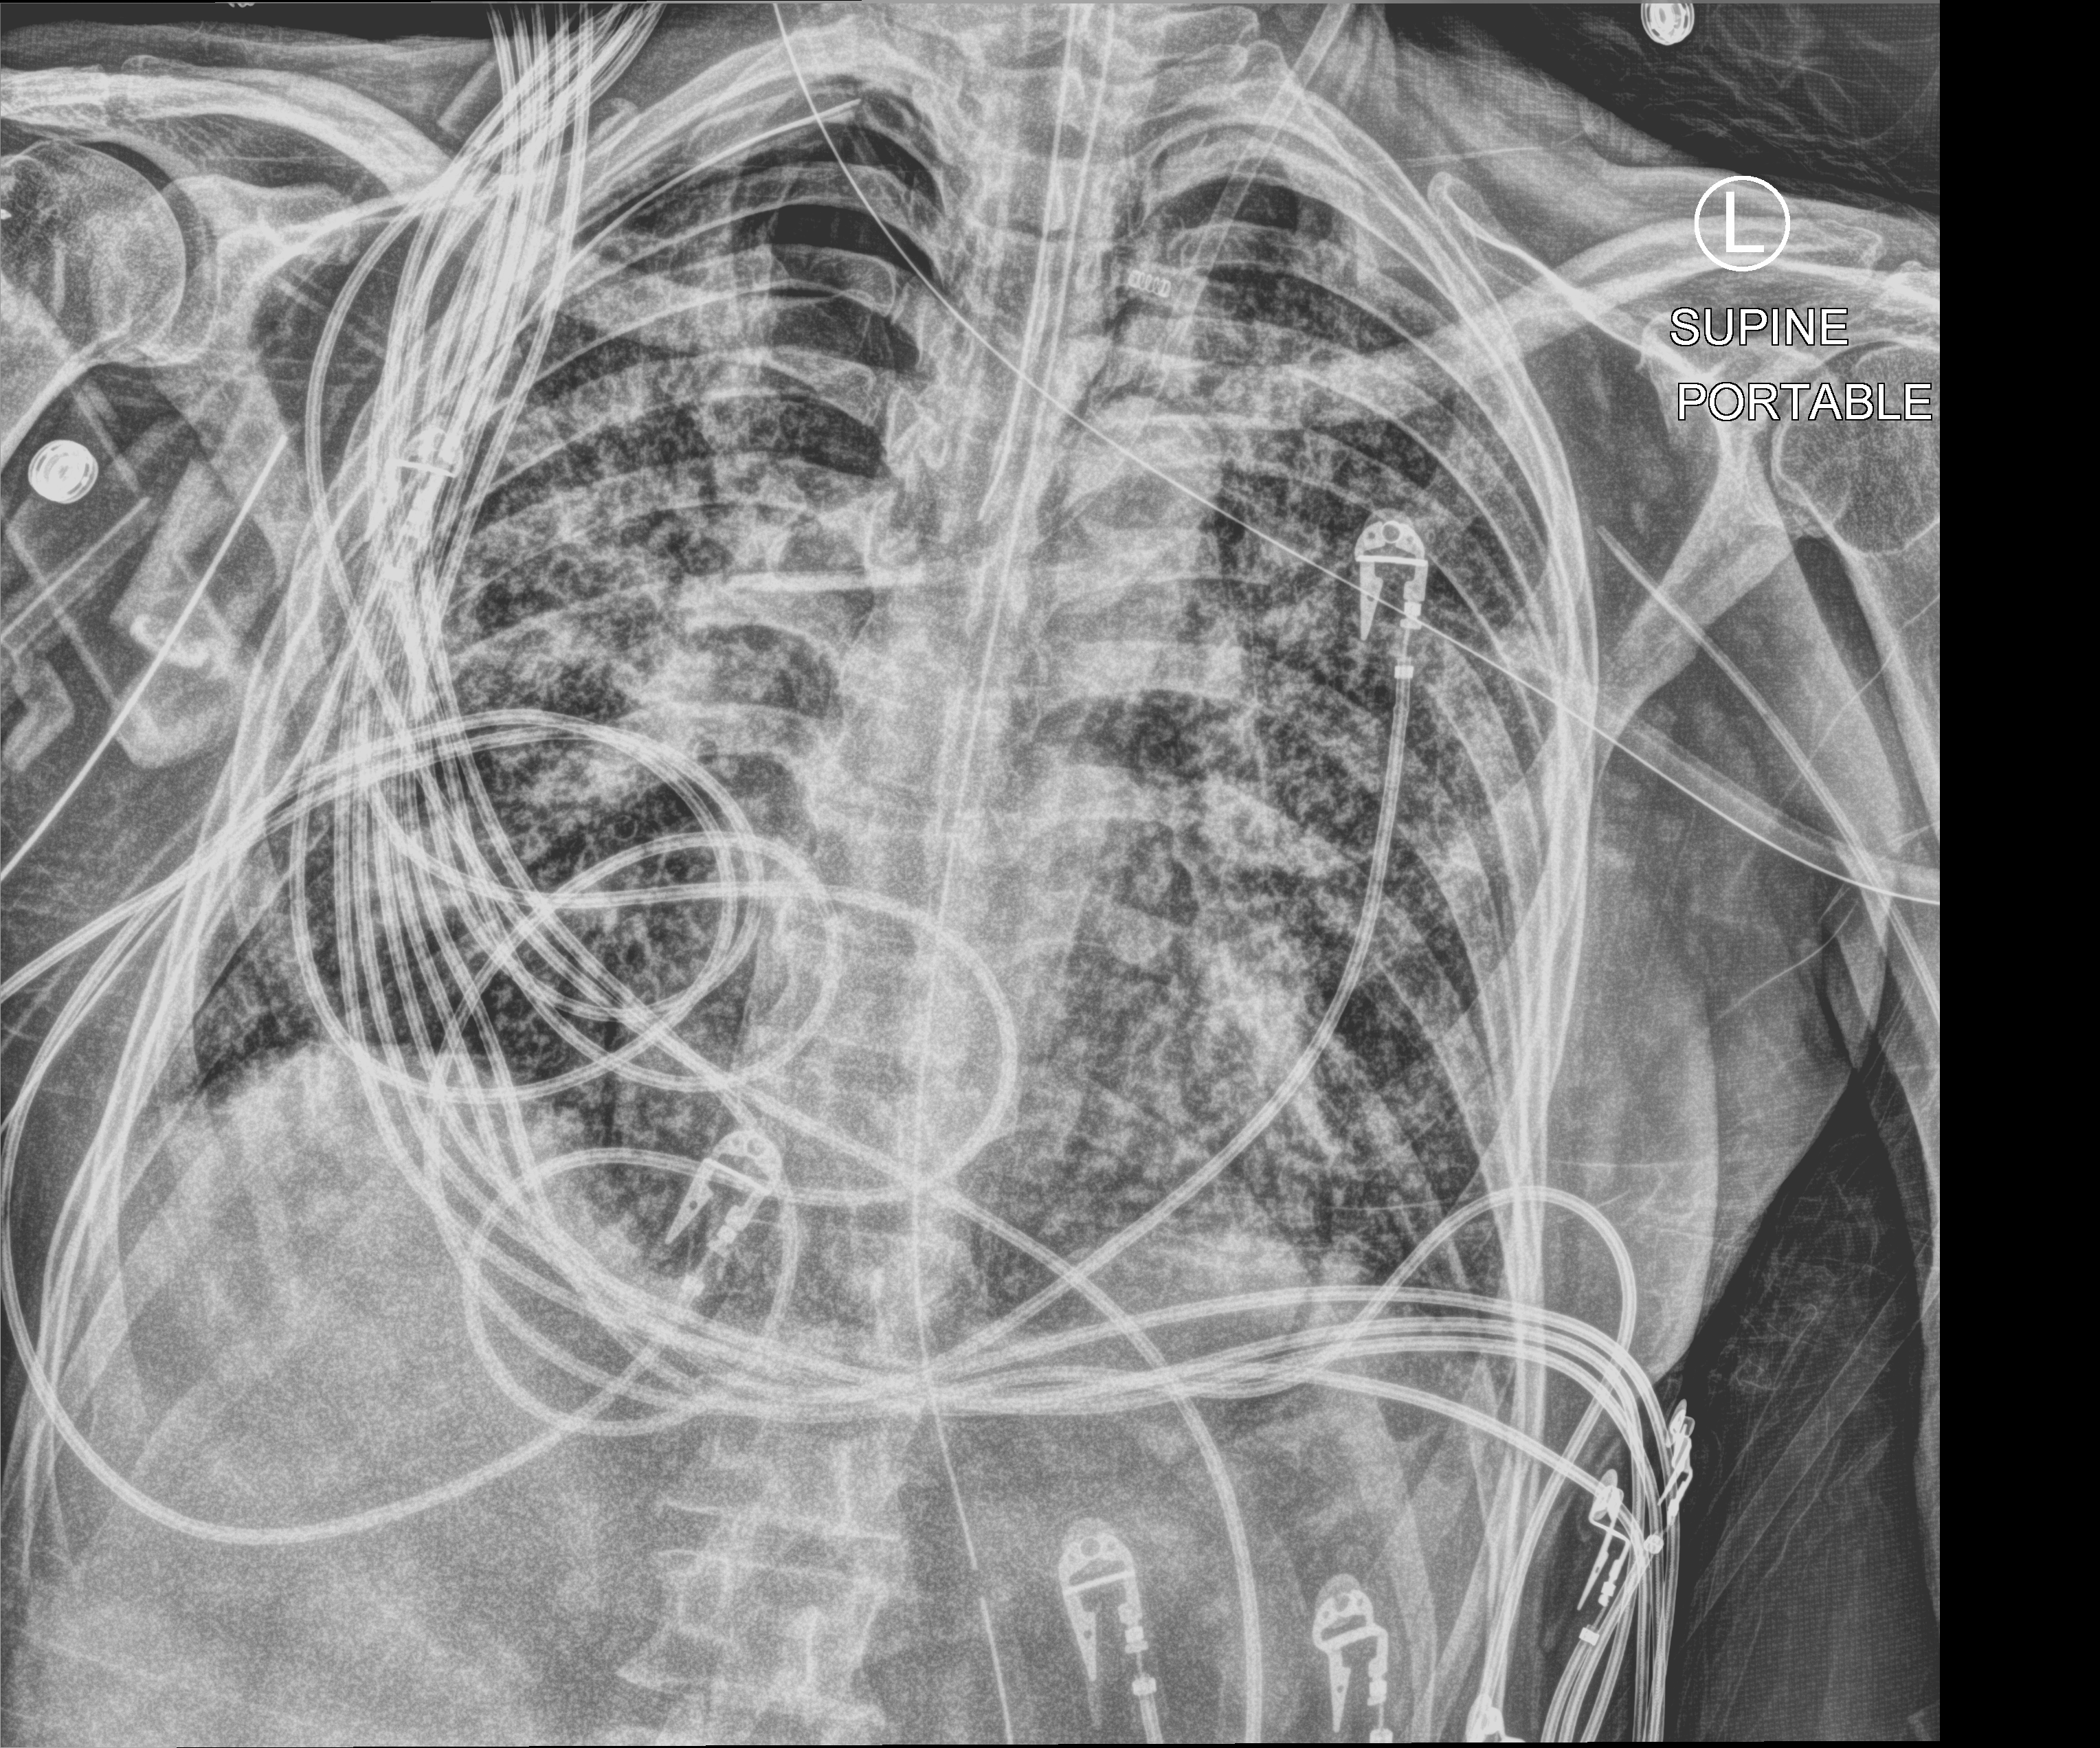
Chest X-ray (portable). Male patient hospitalised with COVID-19, age 60–74 years.
Hospital-stay facts (about this admission, not read from this image; timing relative to this image not recorded): COPD (admission record): no; chronic kidney disease (admission record): no; mechanically ventilated during this hospital stay: yes.